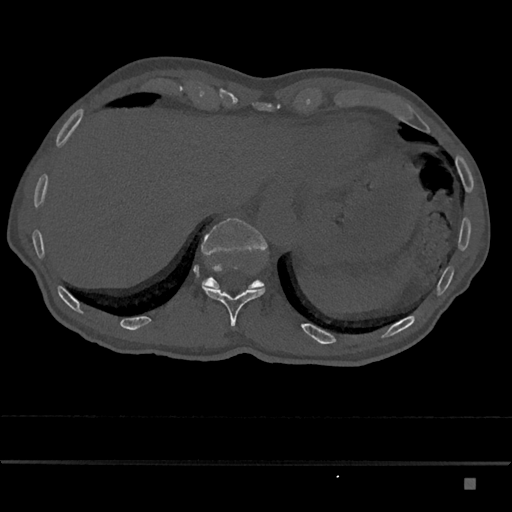
CT including the spine, one axial slice; slice 656 of 797 in the series (ordered by position); reconstruction kernel Br40s/3; 120 kVp; bone window (W 1800 / L 400 HU); 0.5 mm slice thickness; 512 × 512 image matrix, field of view 390 × 390 mm. Male patient, age 72 years. From the clinical record (not read from this slice): primary cancer: prostate.
Structures marked on this image (semi-automatic segmentation, software-assisted and operator-edited):
- T11 vertebra: box from (x=202, y=283) to (x=265, y=327) px
- T12 vertebra: (x=201, y=218)–(x=267, y=290)